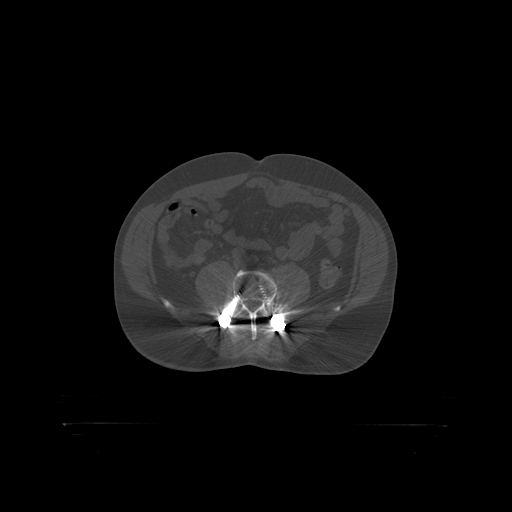
CT including the spine, one axial slice; reconstruction kernel STANDARD; 120 kVp; bone window (W 1800 / L 400 HU); 1.25 mm slice thickness; 512 × 512 image matrix, field of view 650 × 650 mm. Patient: male, 46 years. From the clinical record (not read from this slice): primary cancer: skin.
Structures marked on this image (semi-automatic segmentation, software-assisted and operator-edited):
- L4 vertebra: bounding box (x1, y1, x2, y2) in pixels: (236, 313, 270, 318)
- L5 vertebra: (219, 271, 290, 319)